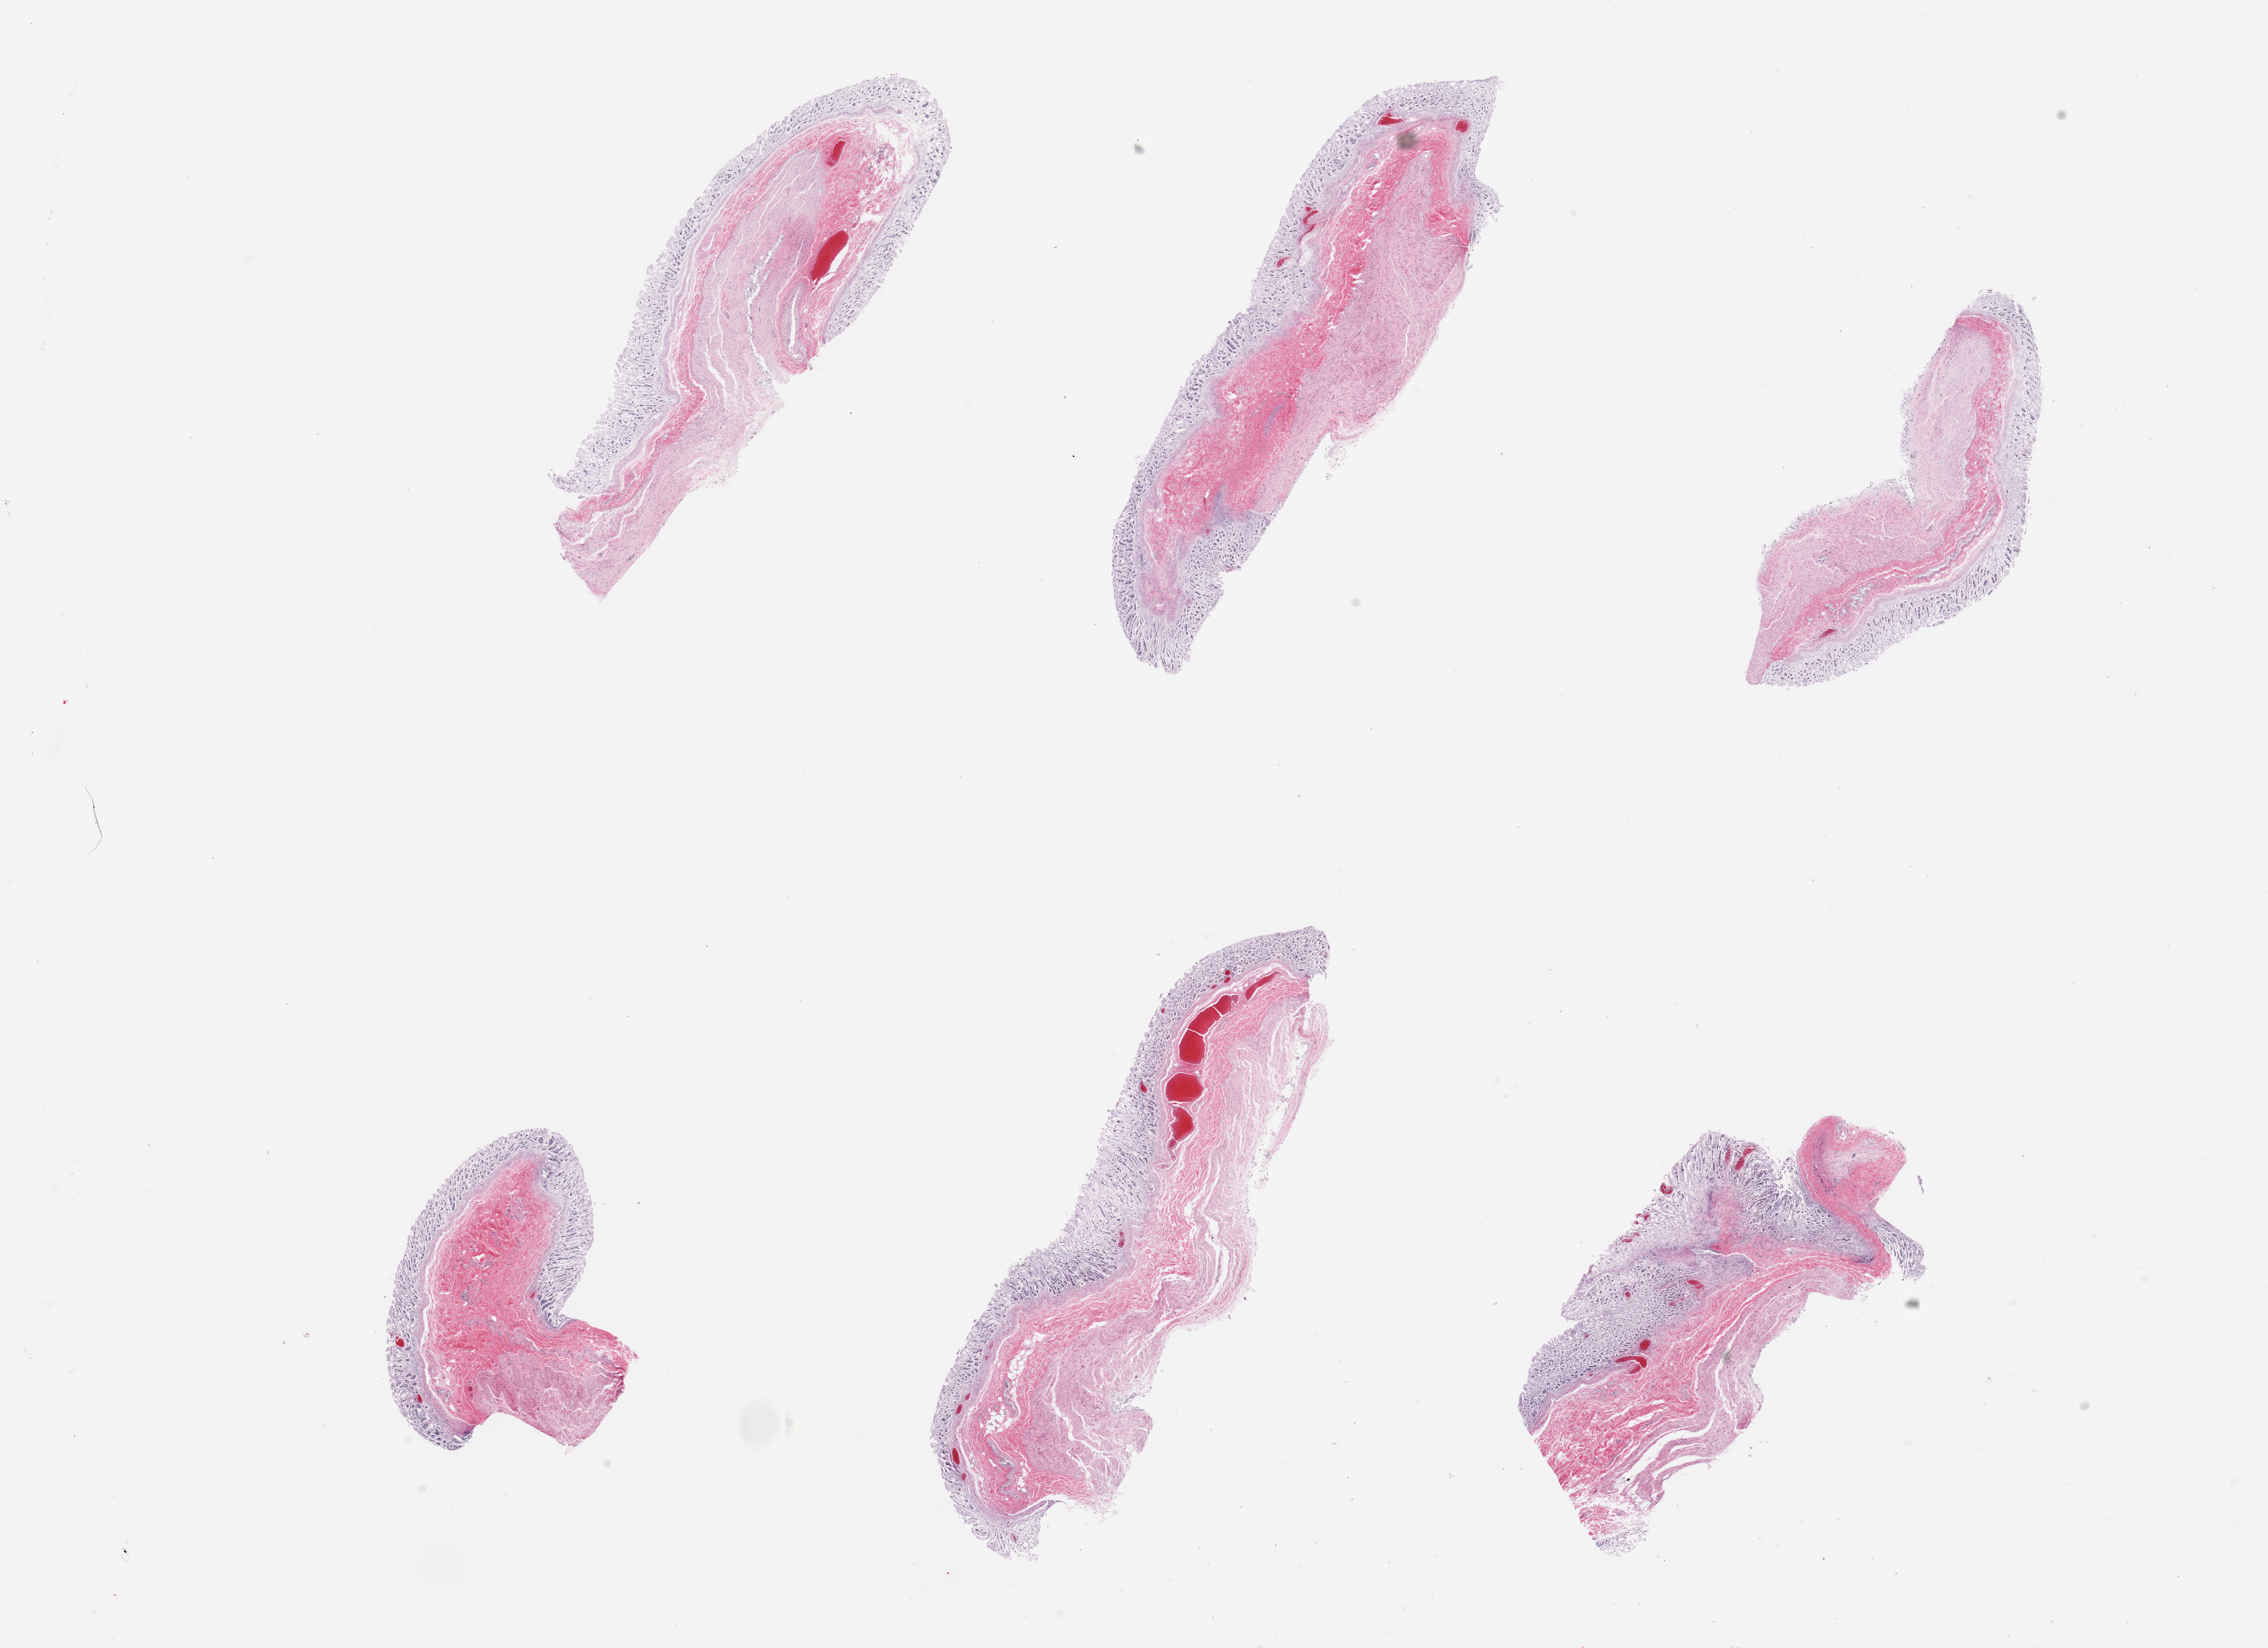
H&E whole-slide image, brightfield, low-resolution overview of the scanned area, about 25.6 x 18.6 mm (slide scanned at 20x), PAXgene-fixed, paraffin-embedded tissue, target tissue: stomach, donor tissue sample. Male donor.
Reviewer comment on this tissue sample: 6 pieces; severely autolyzed full thickness sections.